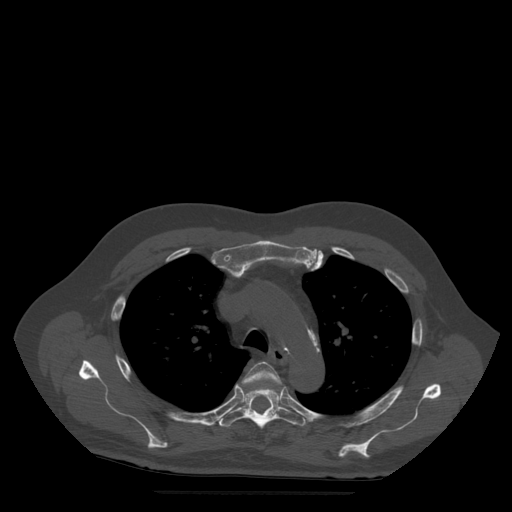
CT including the spine, one axial slice. Position 379 of 522 along the scan axis. Bone window (W 1800 / L 400 HU). 1.25 mm slice thickness. 512 × 512 image matrix. Patient age 72 years. From the clinical record (not read from this slice): primary cancer: prostate.
Structures marked on this image (semi-automatically segmented with operator editing):
- T4 vertebra: box from (x=243, y=362) to (x=282, y=390) px
- T5 vertebra: (x=219, y=387)–(x=306, y=429)